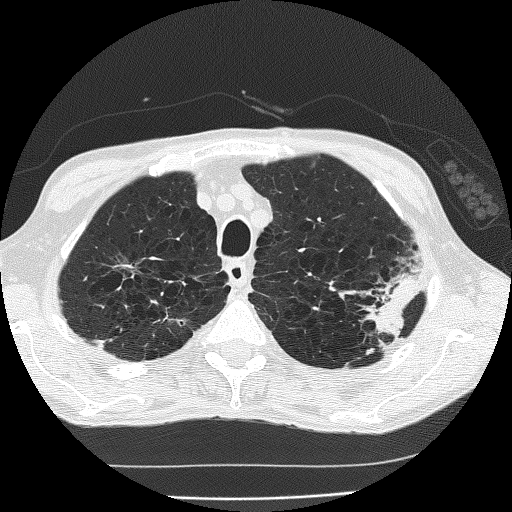
Axial slice from a low-dose chest CT screening exam; second screening round (one year after baseline); lung window (W 1500 / L -600 HU); slice 36 of 185 in the series. Male, age 60 years at enrolment. Current smoker at enrolment.
- Expert reader's lesion annotation, bounding box [x1, y1, x2, y2] px = [346, 263, 426, 340].
- The screening reader recorded 2 non-calcified nodules or masses ≥4 mm on this exam; which of them this box marks is not recorded.
- Later outcome: lung cancer diagnosed 178 days after this screen — bronchiolo-alveolar carcinoma, mucinous, left upper lobe, stage IV (AJCC 6th edition).